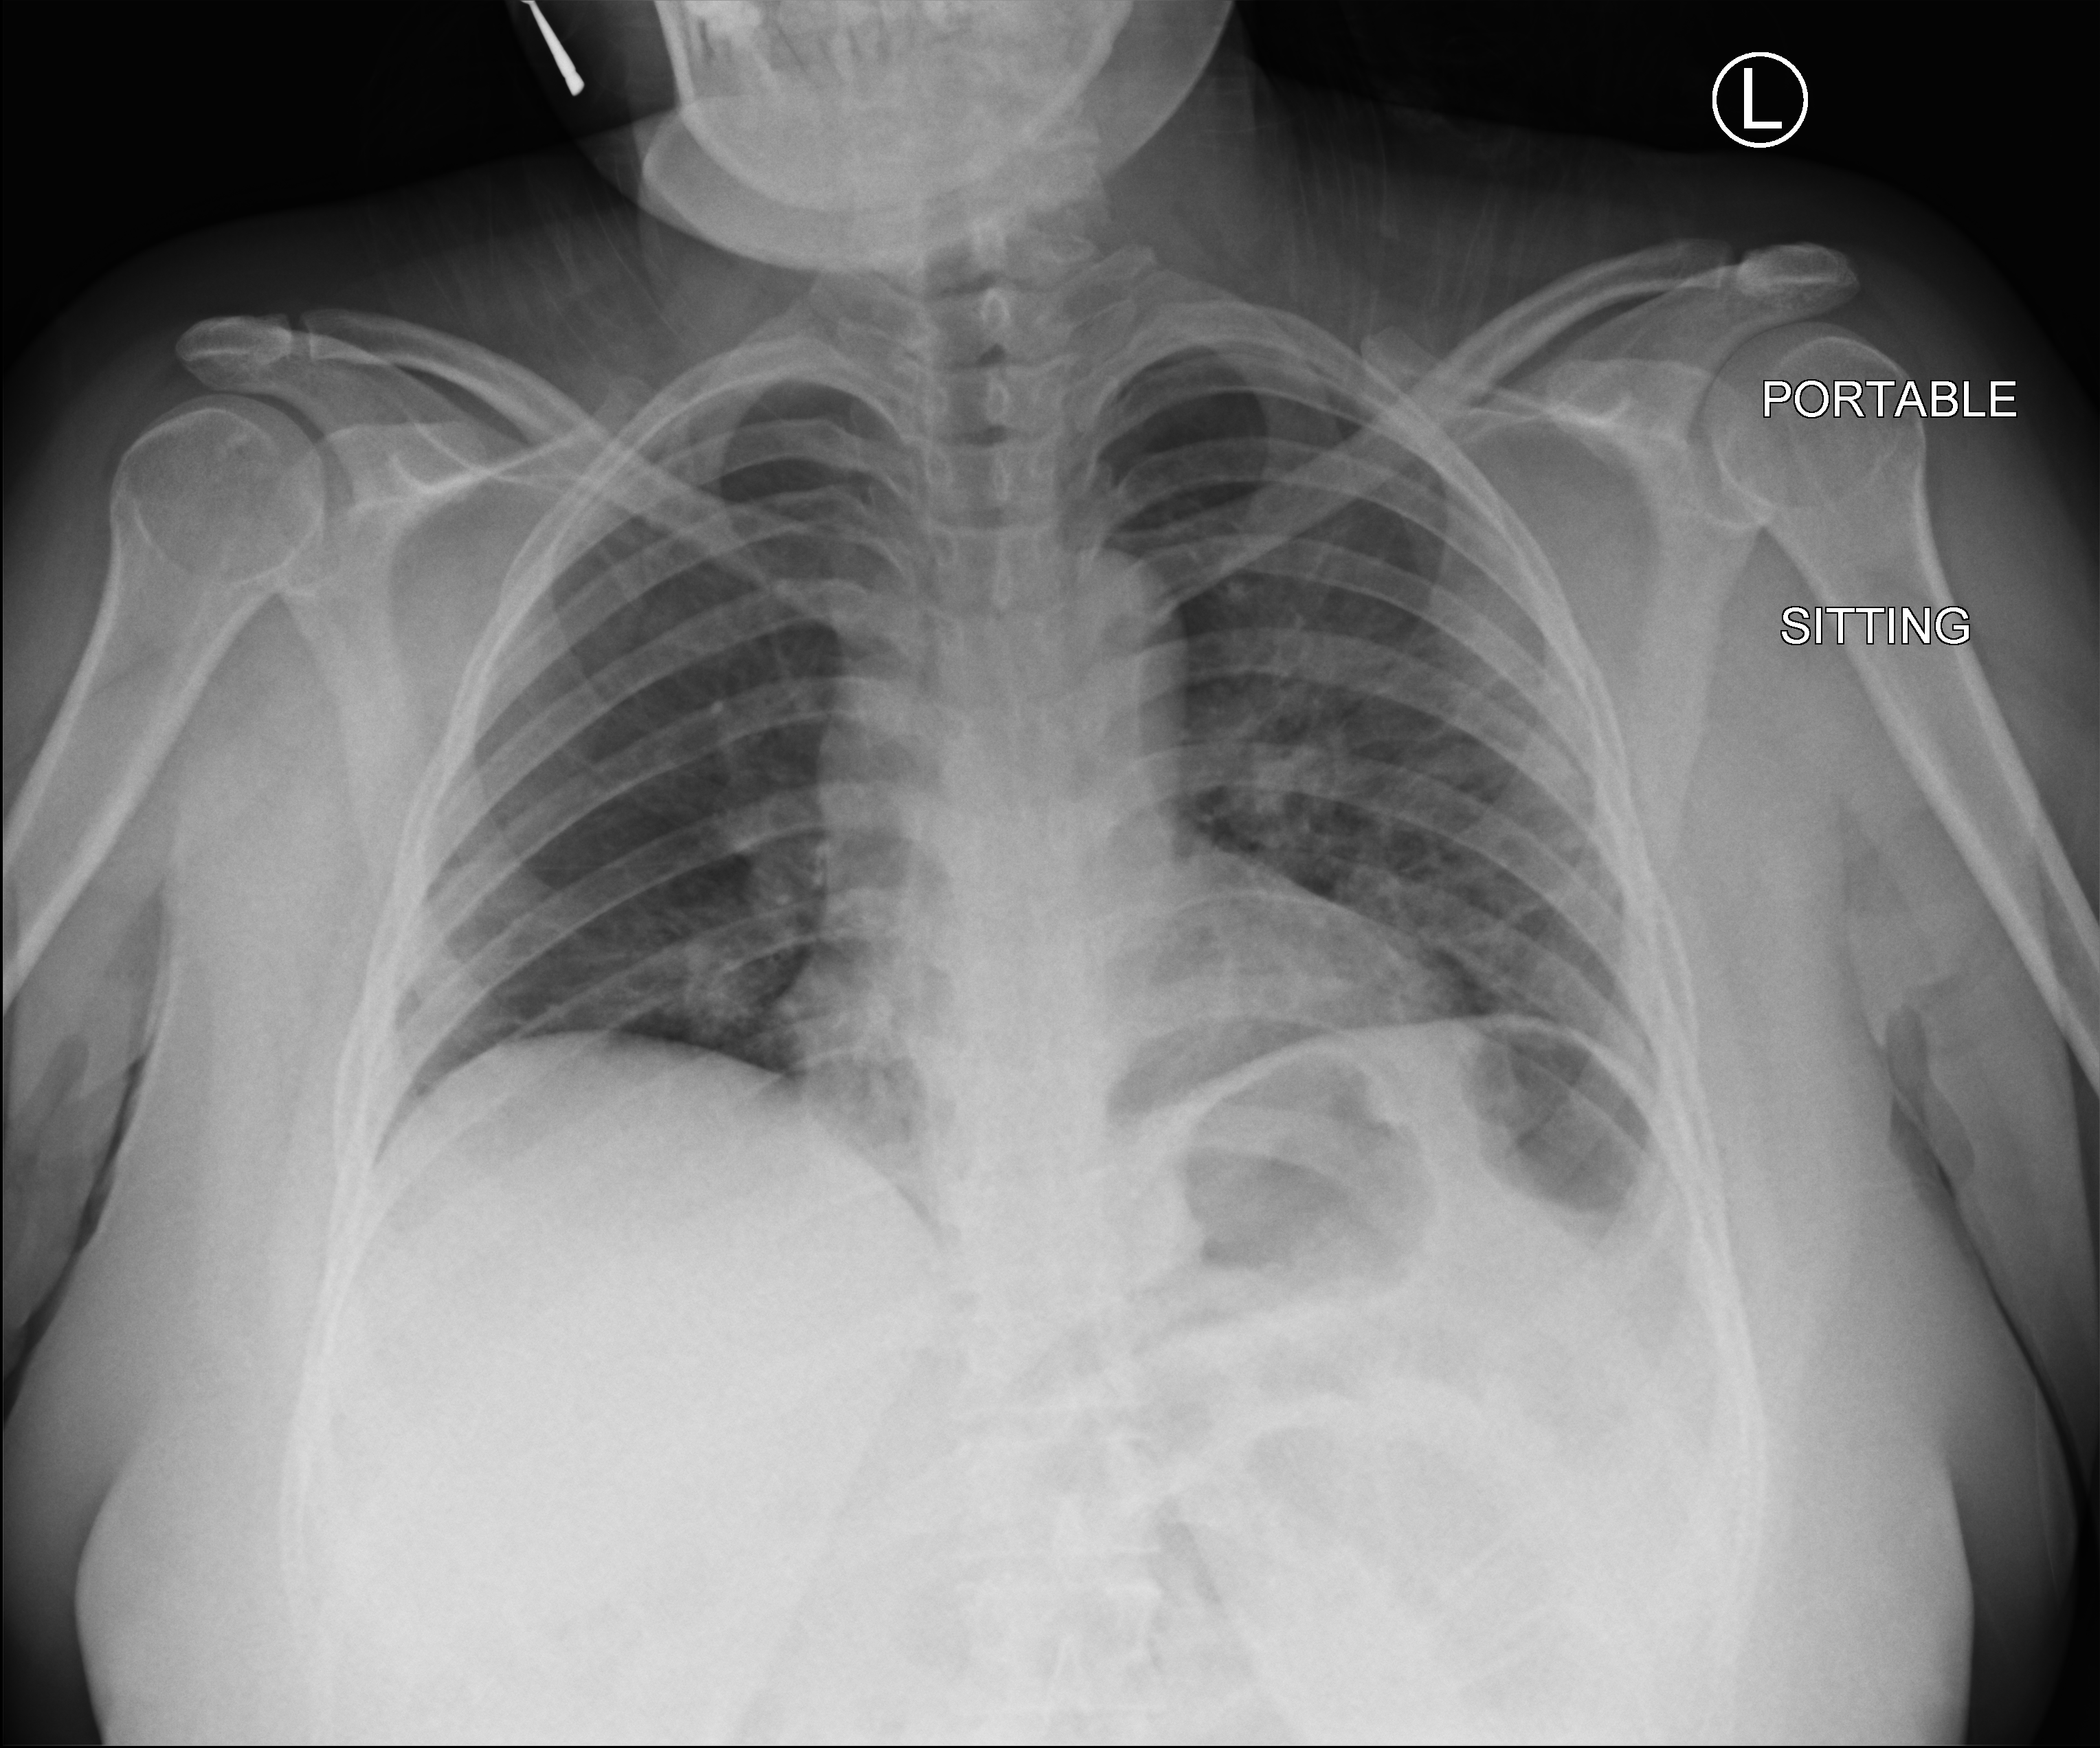
Chest X-ray (portable); anteroposterior (AP) projection. Patient hospitalised with COVID-19; female, aged 18–59 years.
From the hospital-stay record, not from the radiograph (when in the stay this image was taken is not recorded): admitted to intensive care during this hospital stay: no.